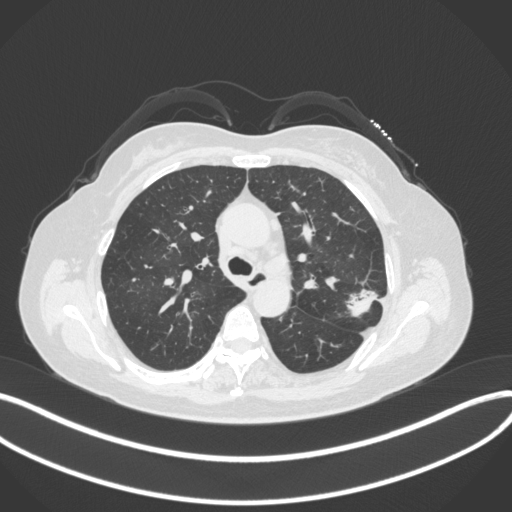
Chest CT, one axial slice; slice 231 of 330 in the series (ordered by position); lung window (W 1500 / L -600 HU); 1 mm slice thickness; 512 × 512 image matrix, field of view 400 × 400 mm. Patient: female, 60 years. From the clinical record (not read from this slice): clinical TNM (as recorded): T1c N0 M0.
Outlined on this slice (rectangle marked by the reading radiologist):
- lung tumour (recorded histology: adenocarcinoma): box from (x=343, y=282) to (x=381, y=321) px